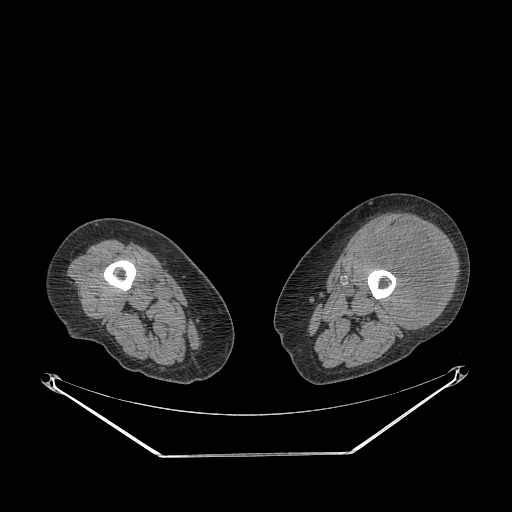
CT of an extremity soft-tissue mass (from a PET/CT study), one axial slice. Slice 214 of 267 in the series (ordered by position). Reconstruction kernel STANDARD. 140 kVp. Soft-tissue window (W 400 / L 40 HU). 512 × 512 image matrix, field of view 500 × 500 mm. Female patient. Case-level facts recorded for this patient, not image findings: histological type: undifferentiated – high grade; grade: high; site of the primary tumour: left thigh.
Outlined on this slice (expert contour drawn on MRI and transferred to this co-registered scan by the dataset authors):
- gross tumour volume including surrounding oedema: bounding box (x1, y1, x2, y2) in pixels: (361, 224, 451, 330)
- gross tumour volume (mass): (365, 226, 449, 330)